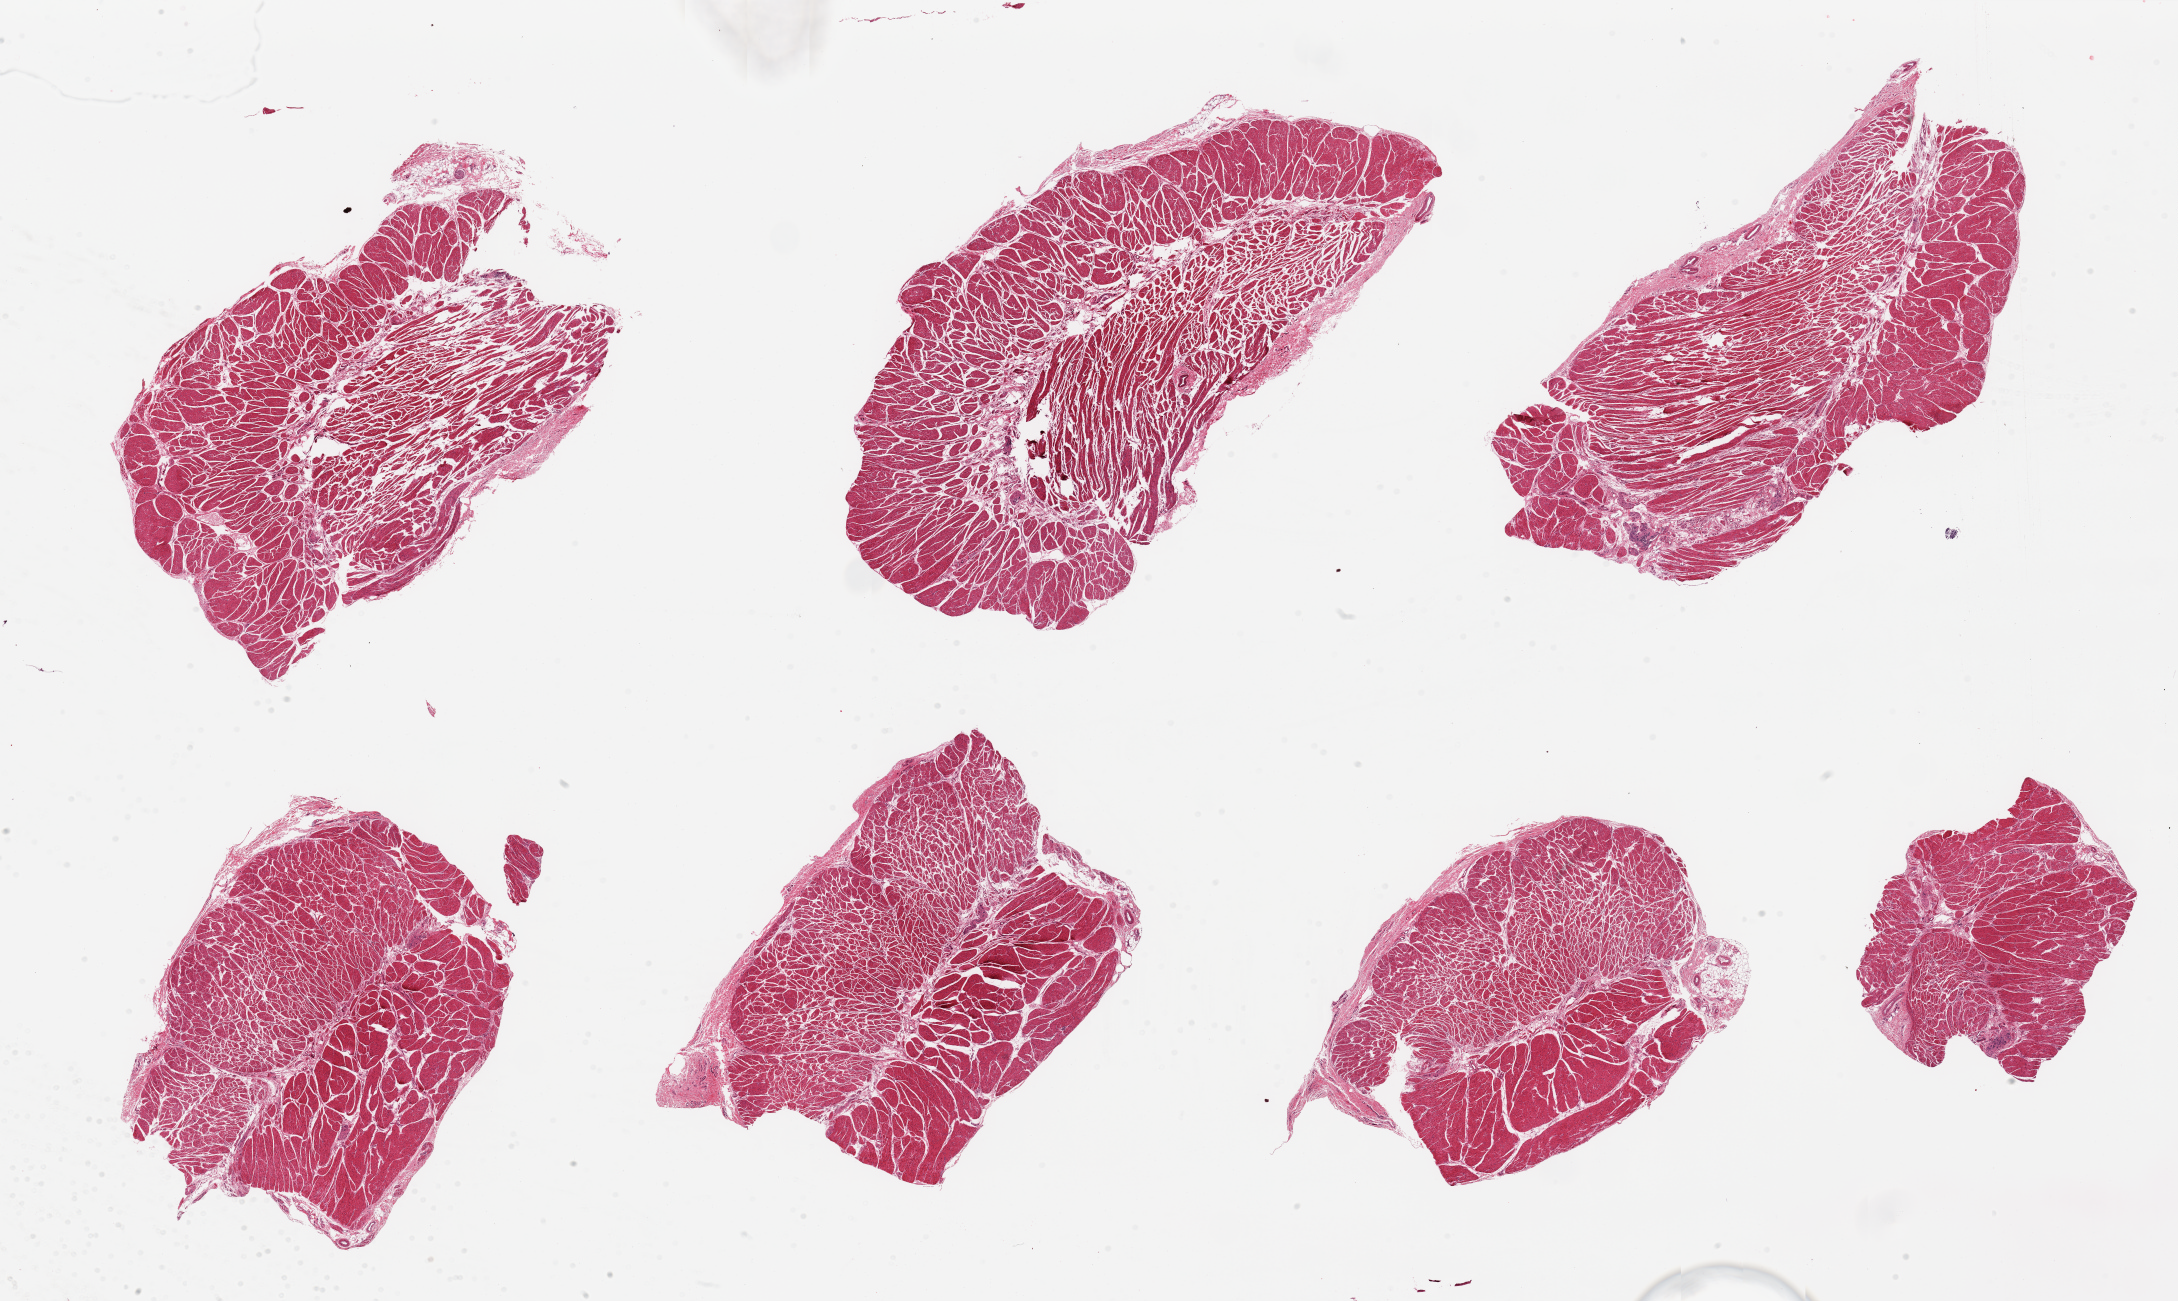
Haematoxylin and eosin whole-slide image, brightfield, a low-resolution overview of the entire scanned area, about 34.5 x 20.6 mm (acquisition: 20x scan), PAXgene-fixed paraffin-embedded (PFPE) section, sampled site (target tissue): esophageal muscle, donor tissue sample. Male donor.
Pathologist's review note for this sample: 7 pieces, all taraget muscularis.